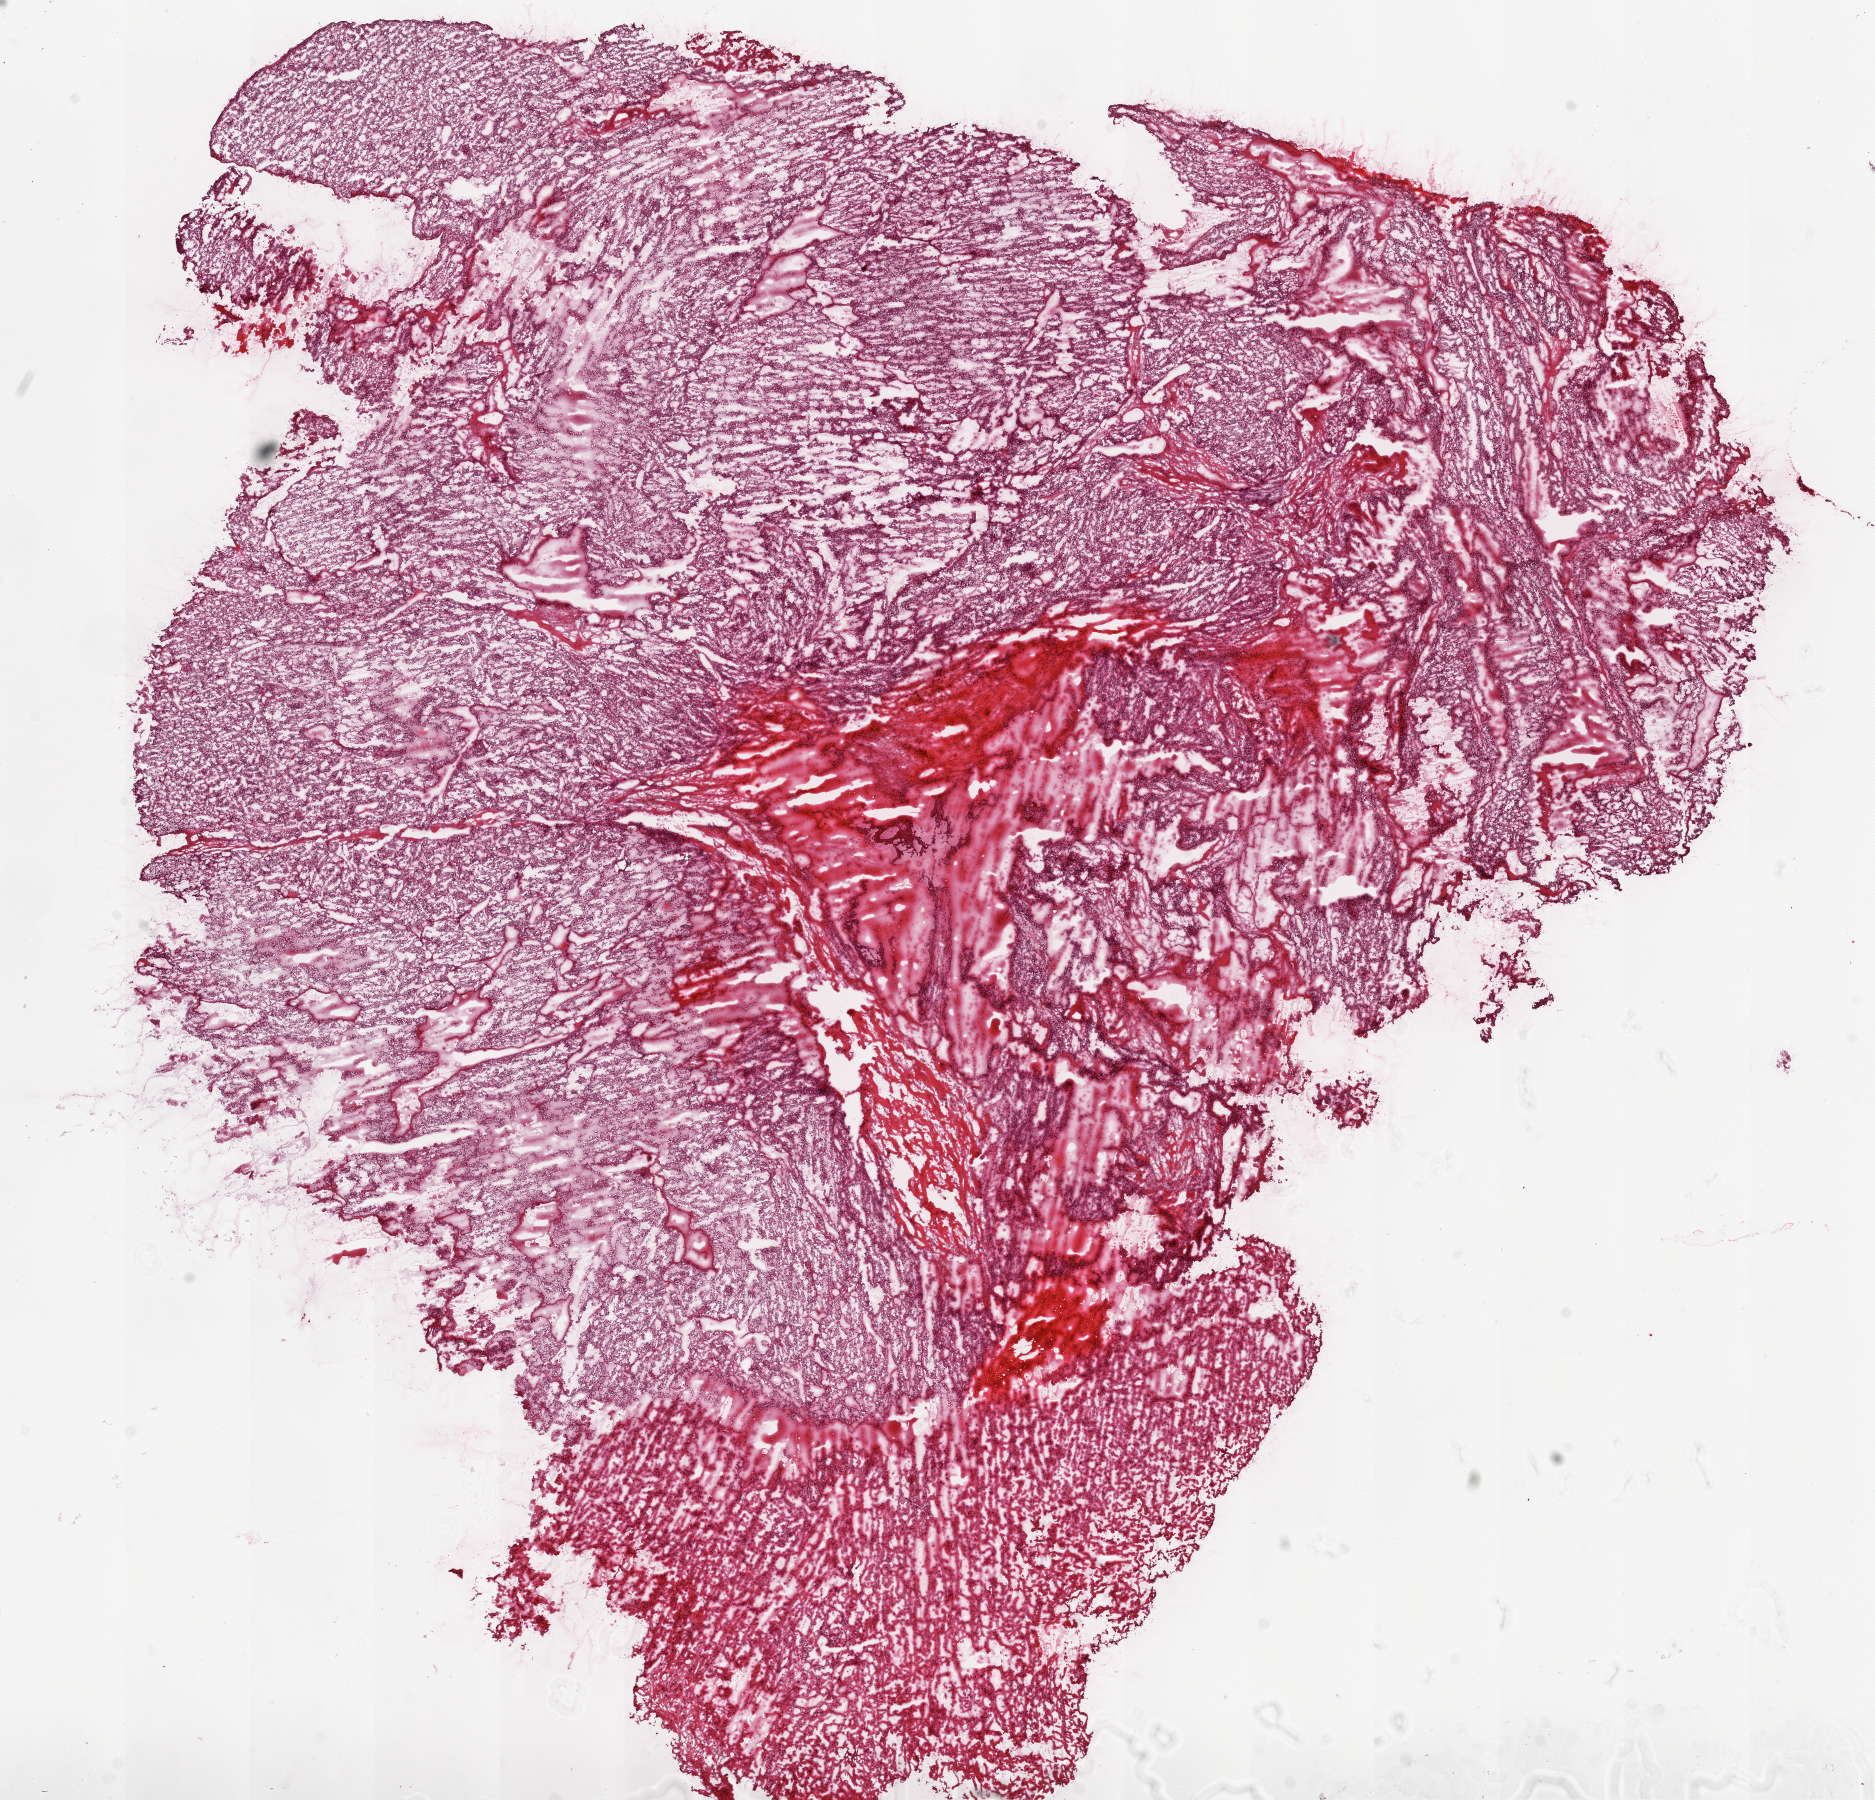
Digitized H&E tissue section (whole slide), shown as a low-resolution overview of the whole scanned area (about 15.0 x 14.4 mm, acquisition: 20x scan). Frozen section from the top of the tissue portion. Primary tumour sample from the kidney. Patient: male, age at initial diagnosis 58 years. Histologic grade: G4 (undifferentiated). Slide review estimates, as recorded: tumour cells 85%, tumour nuclei 85%, normal cells 0%, stromal cells 15%, necrosis 0%.
- AJCC pathologic stage: II
- TNM: T2 N0 M0
- lymph nodes positive (case pathology): 0 of 4 examined
- diagnosis: Clear cell adenocarcinoma, NOS